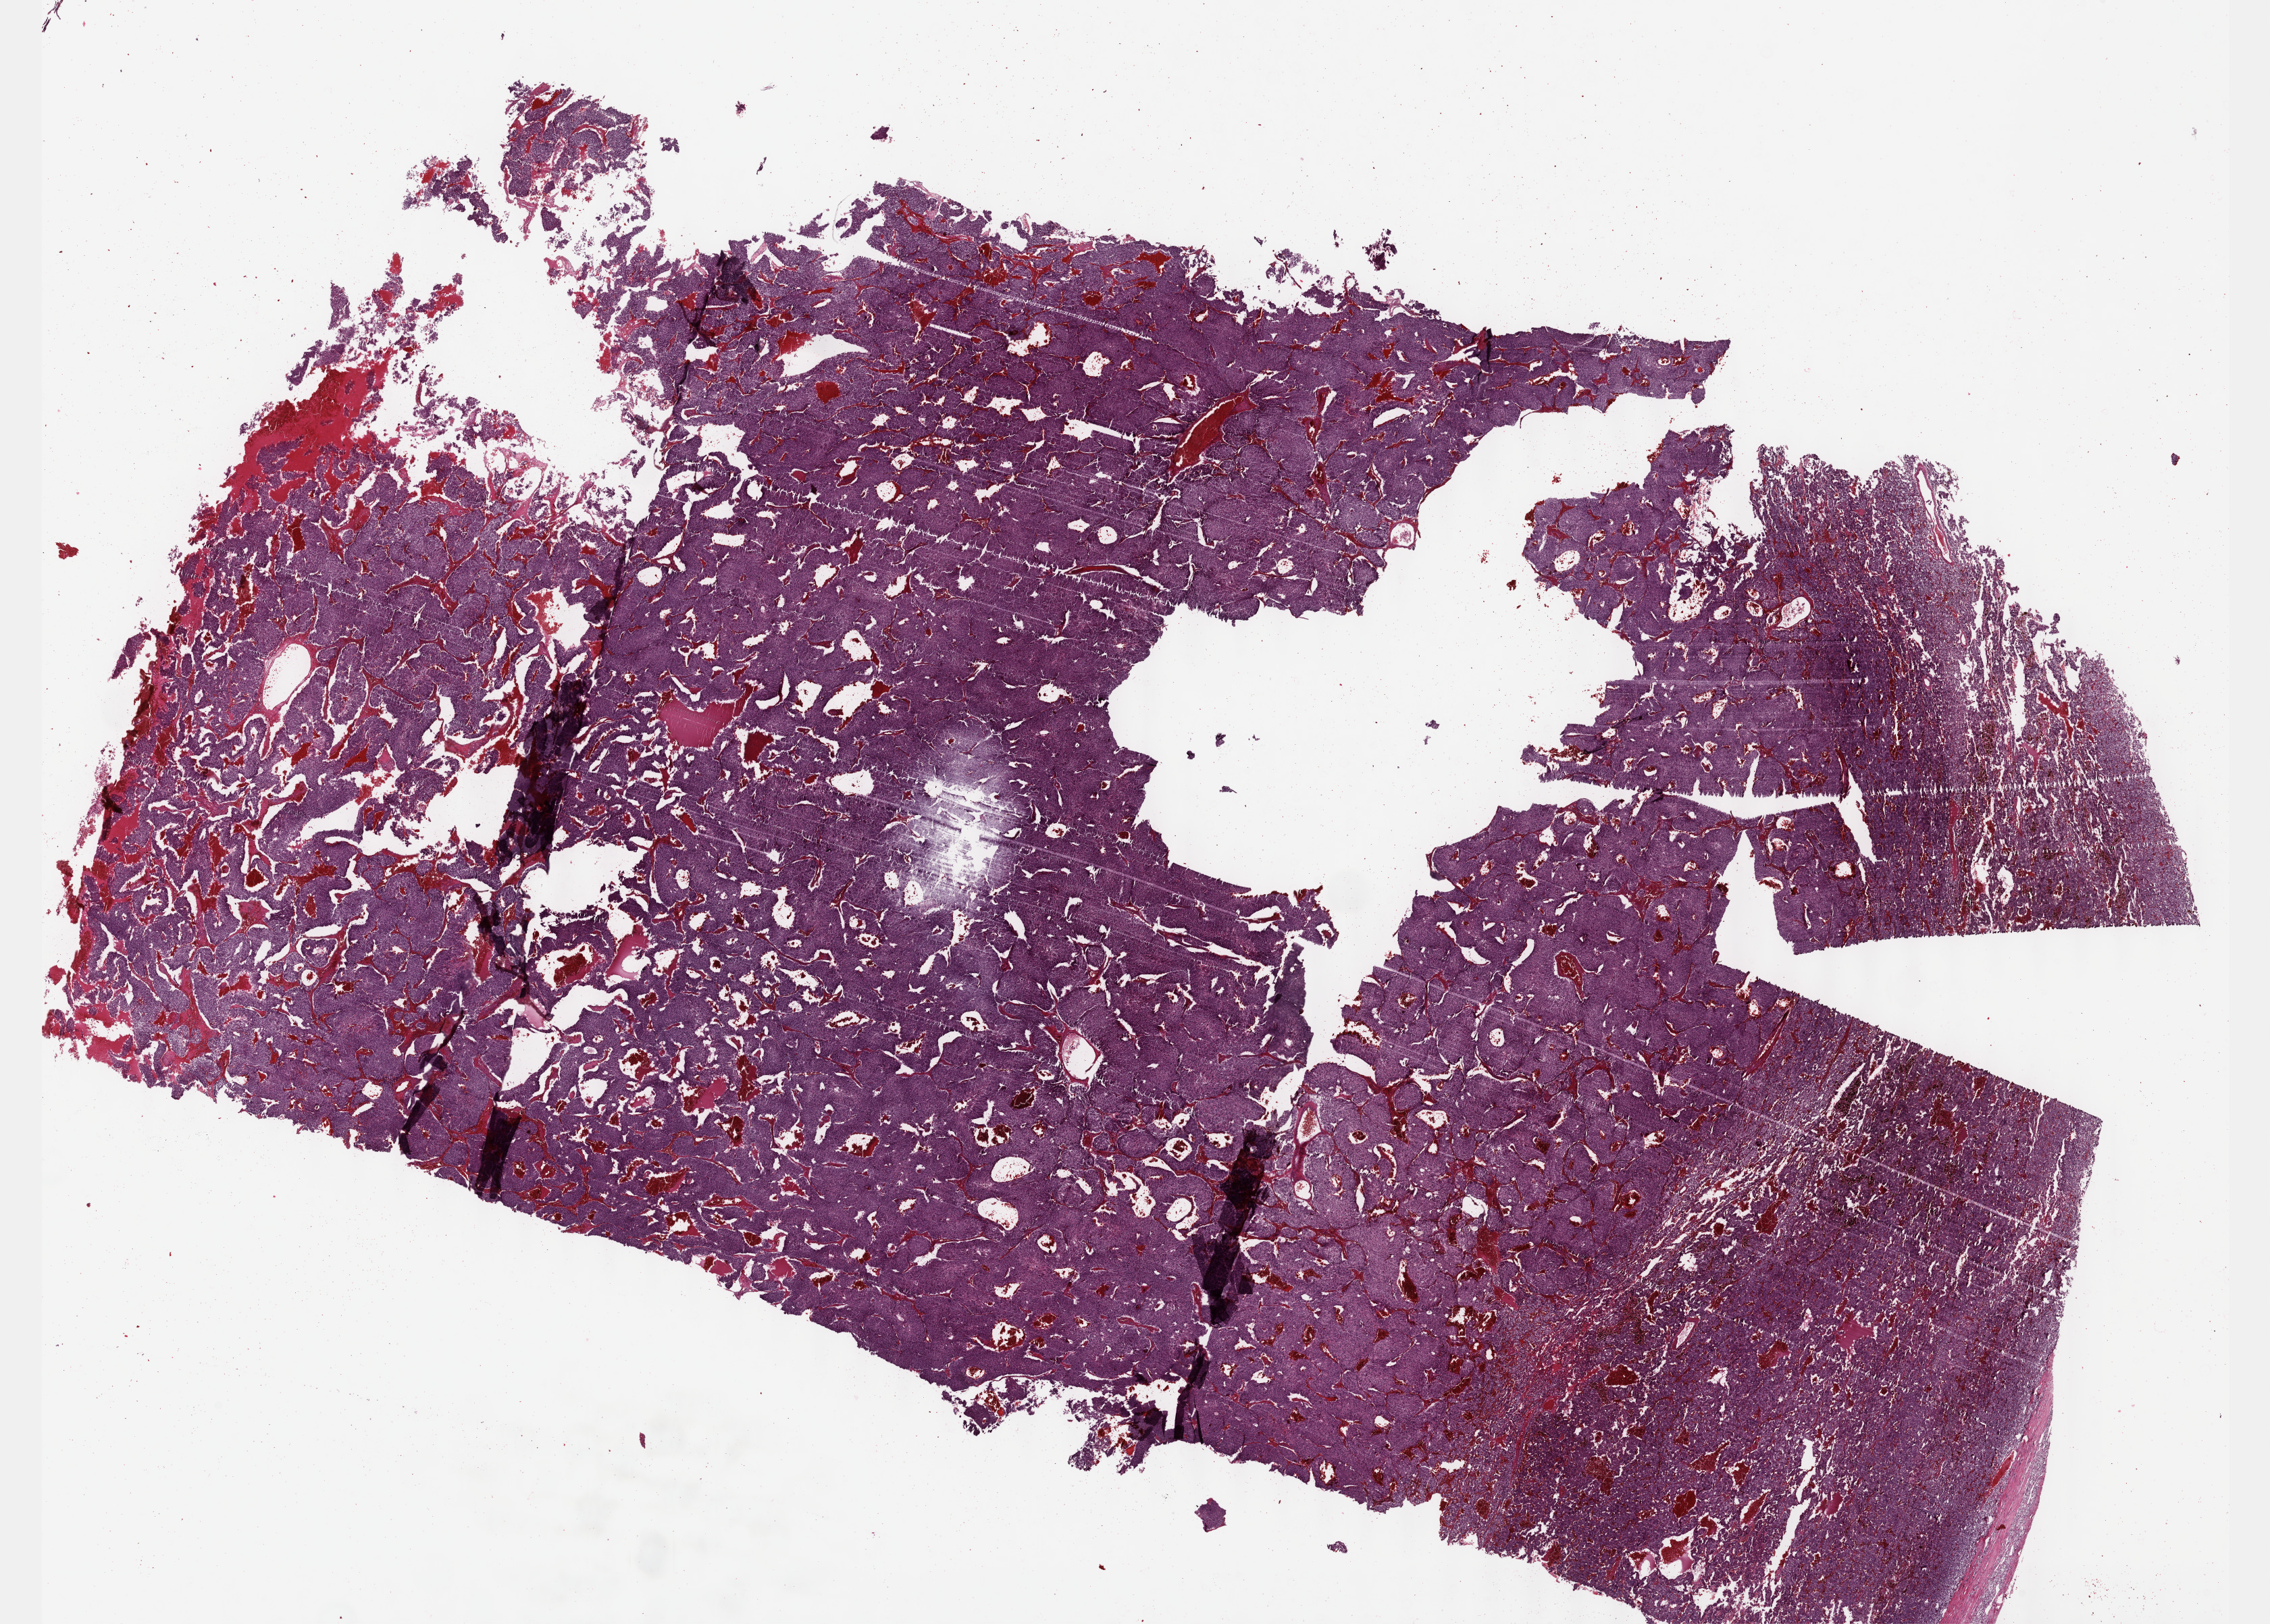
H&E-stained whole-slide image — low-resolution overview of the scanned area, about 27.2 x 19.4 mm (acquisition: 40x scan). FFPE section. Primary tumour sample from the adrenal gland. Male, age 44 years at initial diagnosis.
Pathologic diagnosis: Pheochromocytoma, malignant.